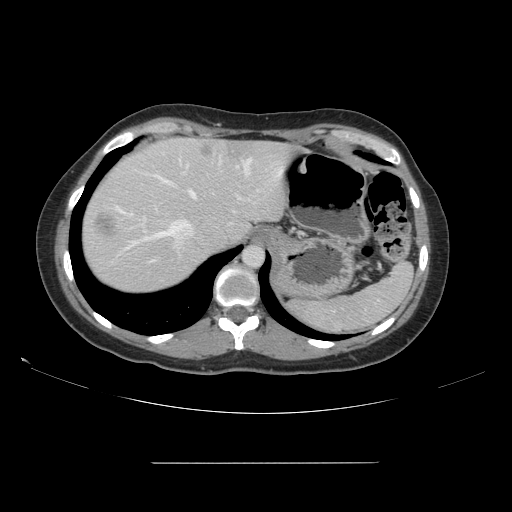
Contrast-enhanced abdominal CT, one axial slice. Slice 123 of 151 in the series (ordered by position). 120 kVp. Intravenous contrast given. Soft-tissue window (W 400 / L 40 HU). 2.5 mm slice thickness. 512 × 512 image matrix, field of view 421 × 421 mm. Female patient, age 46 years. From the clinical record (not read from this slice): diagnosis: colorectal cancer liver metastases, imaged before liver resection; multiple liver metastases: yes; largest metastasis: 3 cm; chemotherapy before resection: no.
Outlined on this slice (outlined manually by an expert reader):
- hepatic veins: bounding box <114,157,253,262> (left, top, right, bottom; pixels)
- liver: <82,139,298,293>
- planned liver remnant (the part of the liver to remain after resection): <94,140,297,247>
- portal vein (with intrahepatic branches): <238,197,240,199>
- liver metastasis: <95,215,115,237>
- liver metastasis: <202,146,213,157>